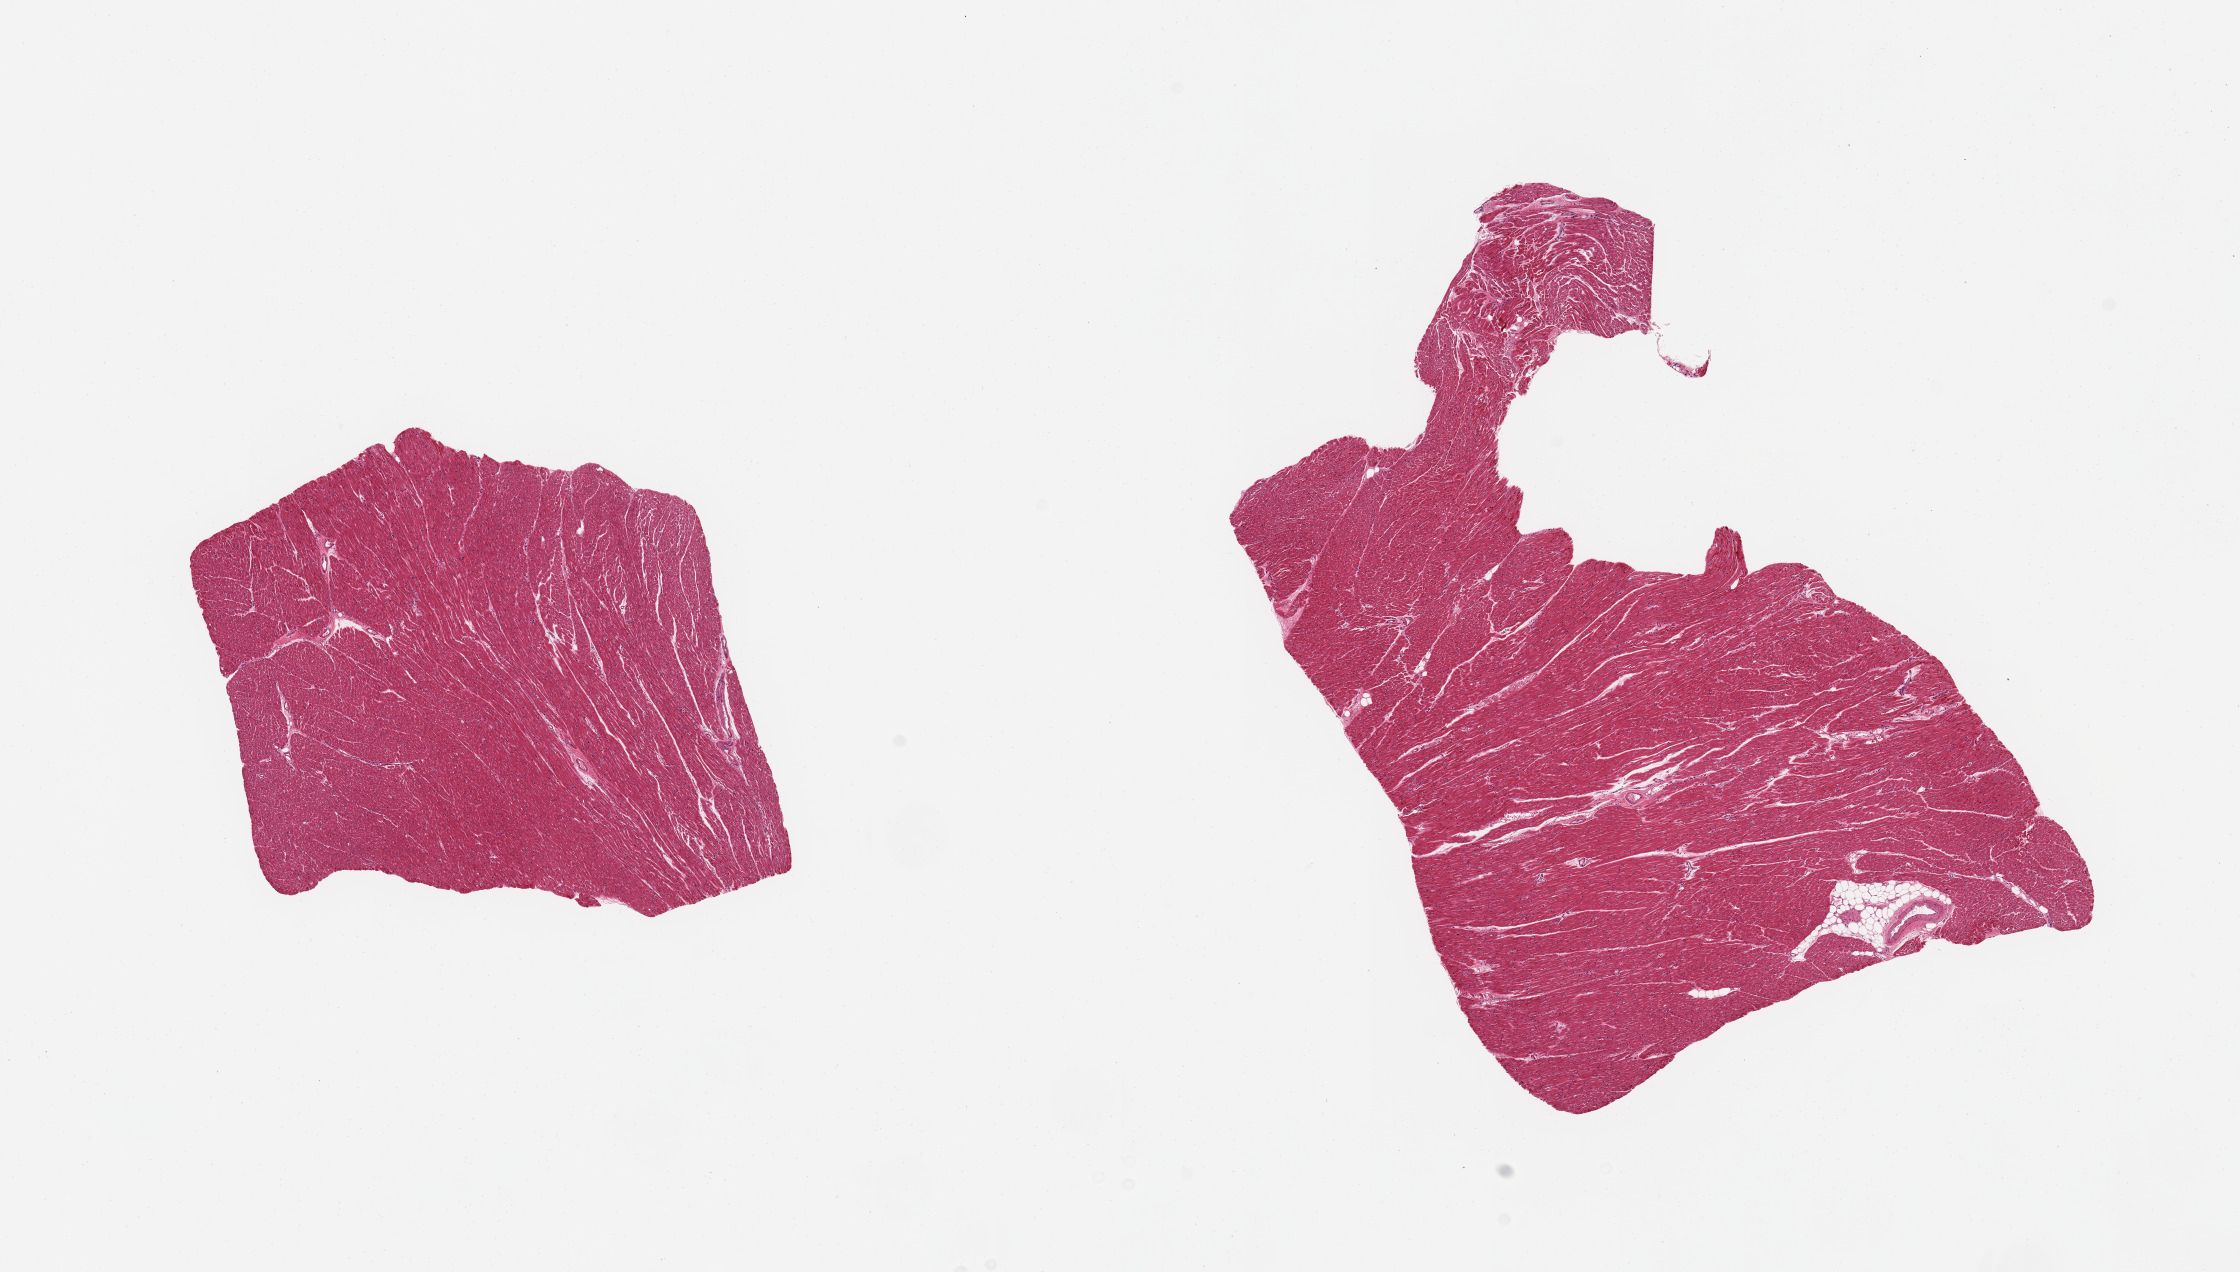
Whole-slide image, hematoxylin and eosin (H&E) stain, whole scanned area (about 17.7 x 10.1 mm) shown as a low-resolution overview; PAXgene-fixed, paraffin-embedded tissue; target tissue: heart; tissue donor sample. Donor sex: male.
Reviewer comment on this tissue sample: 2 pieces; well preserved, no lesions or signs of ischemia.